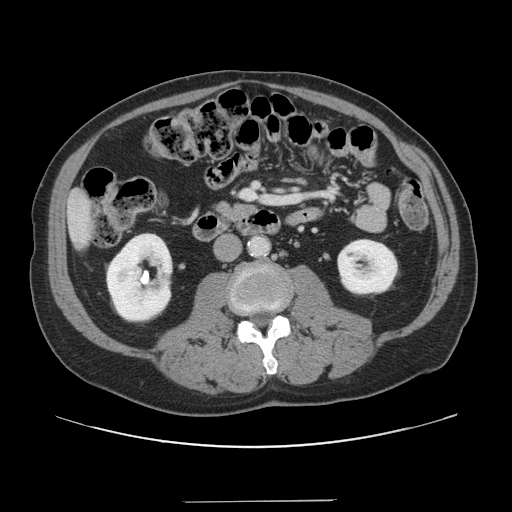
Contrast-enhanced abdominal CT, one axial slice. Position 39 of 151 along the scan axis. Intravenous contrast given. Soft-tissue window (W 400 / L 40 HU). 512 × 512 image matrix, field of view 399 × 399 mm. Male patient, age 63 years. Case-level facts recorded for this patient, not image findings: diagnosis: colorectal cancer liver metastases, imaged before liver resection; multiple liver metastases: no; largest metastasis: 2.1 cm; disease in both lobes: no.
Outlined on this slice (manually delineated by an expert):
- liver: bounding box (x1, y1, x2, y2) in pixels: (69, 190, 94, 247)
- planned liver remnant (the part of the liver to remain after resection): (69, 190, 94, 248)
- portal vein (with intrahepatic branches): (241, 190, 273, 202)